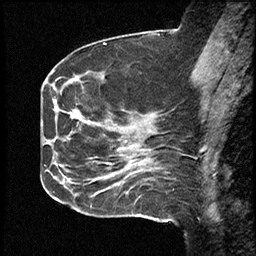
Breast MRI (dynamic contrast-enhanced), one sagittal slice. Slice 20 of 46 in the series (ordered by position). Dynamic contrast-enhanced study with each time point stored as its own series, time point 2 of 4 at this slice position (early post-contrast, ordered by acquisition time). 1.5 T. TE 4.2 ms, TR 18.3 ms. 3 mm slice thickness. 256 × 256 image matrix, field of view 200 × 200 mm. Case-level facts recorded for this patient, not image findings: setting: breast cancer imaged before/during neoadjuvant chemotherapy; receptor status: HR-positive, HER2-negative.
Outlined on this slice (semi-automatic segmentation, software-assisted and operator-edited):
- analysis volume of interest (the breast-tissue region the enhancement analysis was run in; not a lesion): box from (x=64, y=72) to (x=111, y=209) px
- tumour enhancement mask (voxels above the 100 % enhancement threshold inside the analysis volume of interest): (x=75, y=112)–(x=77, y=114)